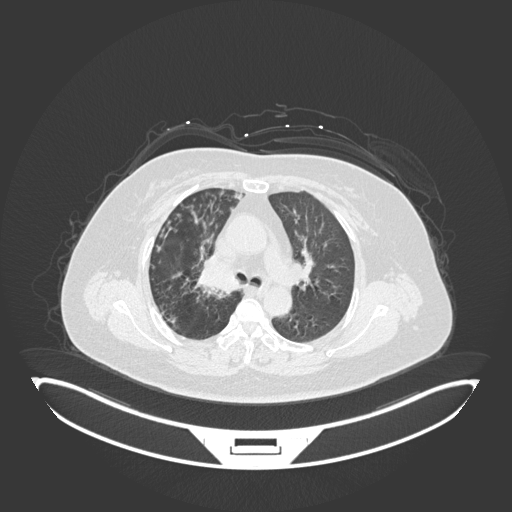
Chest CT, one axial slice. Position 116 of 245 along the scan axis. Reconstruction kernel B30f. Lung window (W 1500 / L -600 HU). 1 mm slice thickness. 512 × 512 image matrix, field of view 500 × 500 mm. Patient: female, 60 years. Case-level facts recorded for this patient, not image findings: clinical TNM (as recorded): T1c N0 M0.
Structures marked on this image (rectangle marked by the reading radiologist):
- lung tumour (recorded histology: squamous cell carcinoma): bounding box <194,257,246,298> (left, top, right, bottom; pixels)